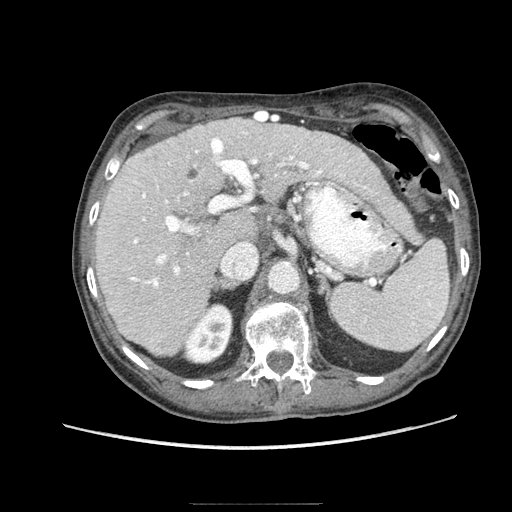
Contrast-enhanced abdominal CT (liver protocol), one axial slice. Slice 53 of 83 in the series (ordered by position). 140 kVp. Soft-tissue window (W 400 / L 40 HU). 512 × 512 image matrix, field of view 360 × 360 mm. Case-level facts recorded for this patient, not image findings: diagnosis: hepatocellular carcinoma (patient treated with transarterial chemoembolisation; whether this scan precedes or follows treatment is not stated here); TNM stage (as recorded): Stage-I; Child-Pugh class: A; tumour differentiation: moderately differentiated; tumour nodularity: uninodular.
Annotated regions visible in this slice (semi-automatically segmented with operator editing):
- liver parenchyma outside the tumour (the mass and vessels are separate outlines, so this box may not span the whole liver): bounding box [x1, y1, x2, y2] px = [94, 118, 382, 356]
- mass: [151, 333, 182, 356]
- liver vessels: [130, 132, 341, 288]